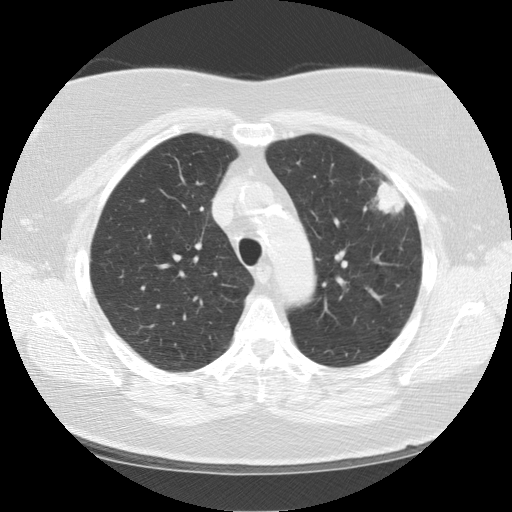
Axial slice from a low-dose chest CT screening exam, baseline annual screen, lung window (W 1500 / L -600 HU), 2.5 mm slice thickness, slice 33 of 130 in the series, 512 × 512 image matrix. Female, age 67 years at enrolment. Former smoker at enrolment.
• Expert-annotated lung lesion, bounding box [x1, y1, x2, y2] px = [349, 162, 420, 228].
• Reader record for this screening exam (exam-level; its link to the box is not recorded): non-calcified nodule or mass ≥4 mm, left upper lobe, 28 × 19 mm, soft tissue attenuation.
• Official screen result: positive, change unspecified: nodule(s) >= 4 mm or enlarging nodule(s), mass(es), or other non-specific abnormalities suspicious for lung cancer.